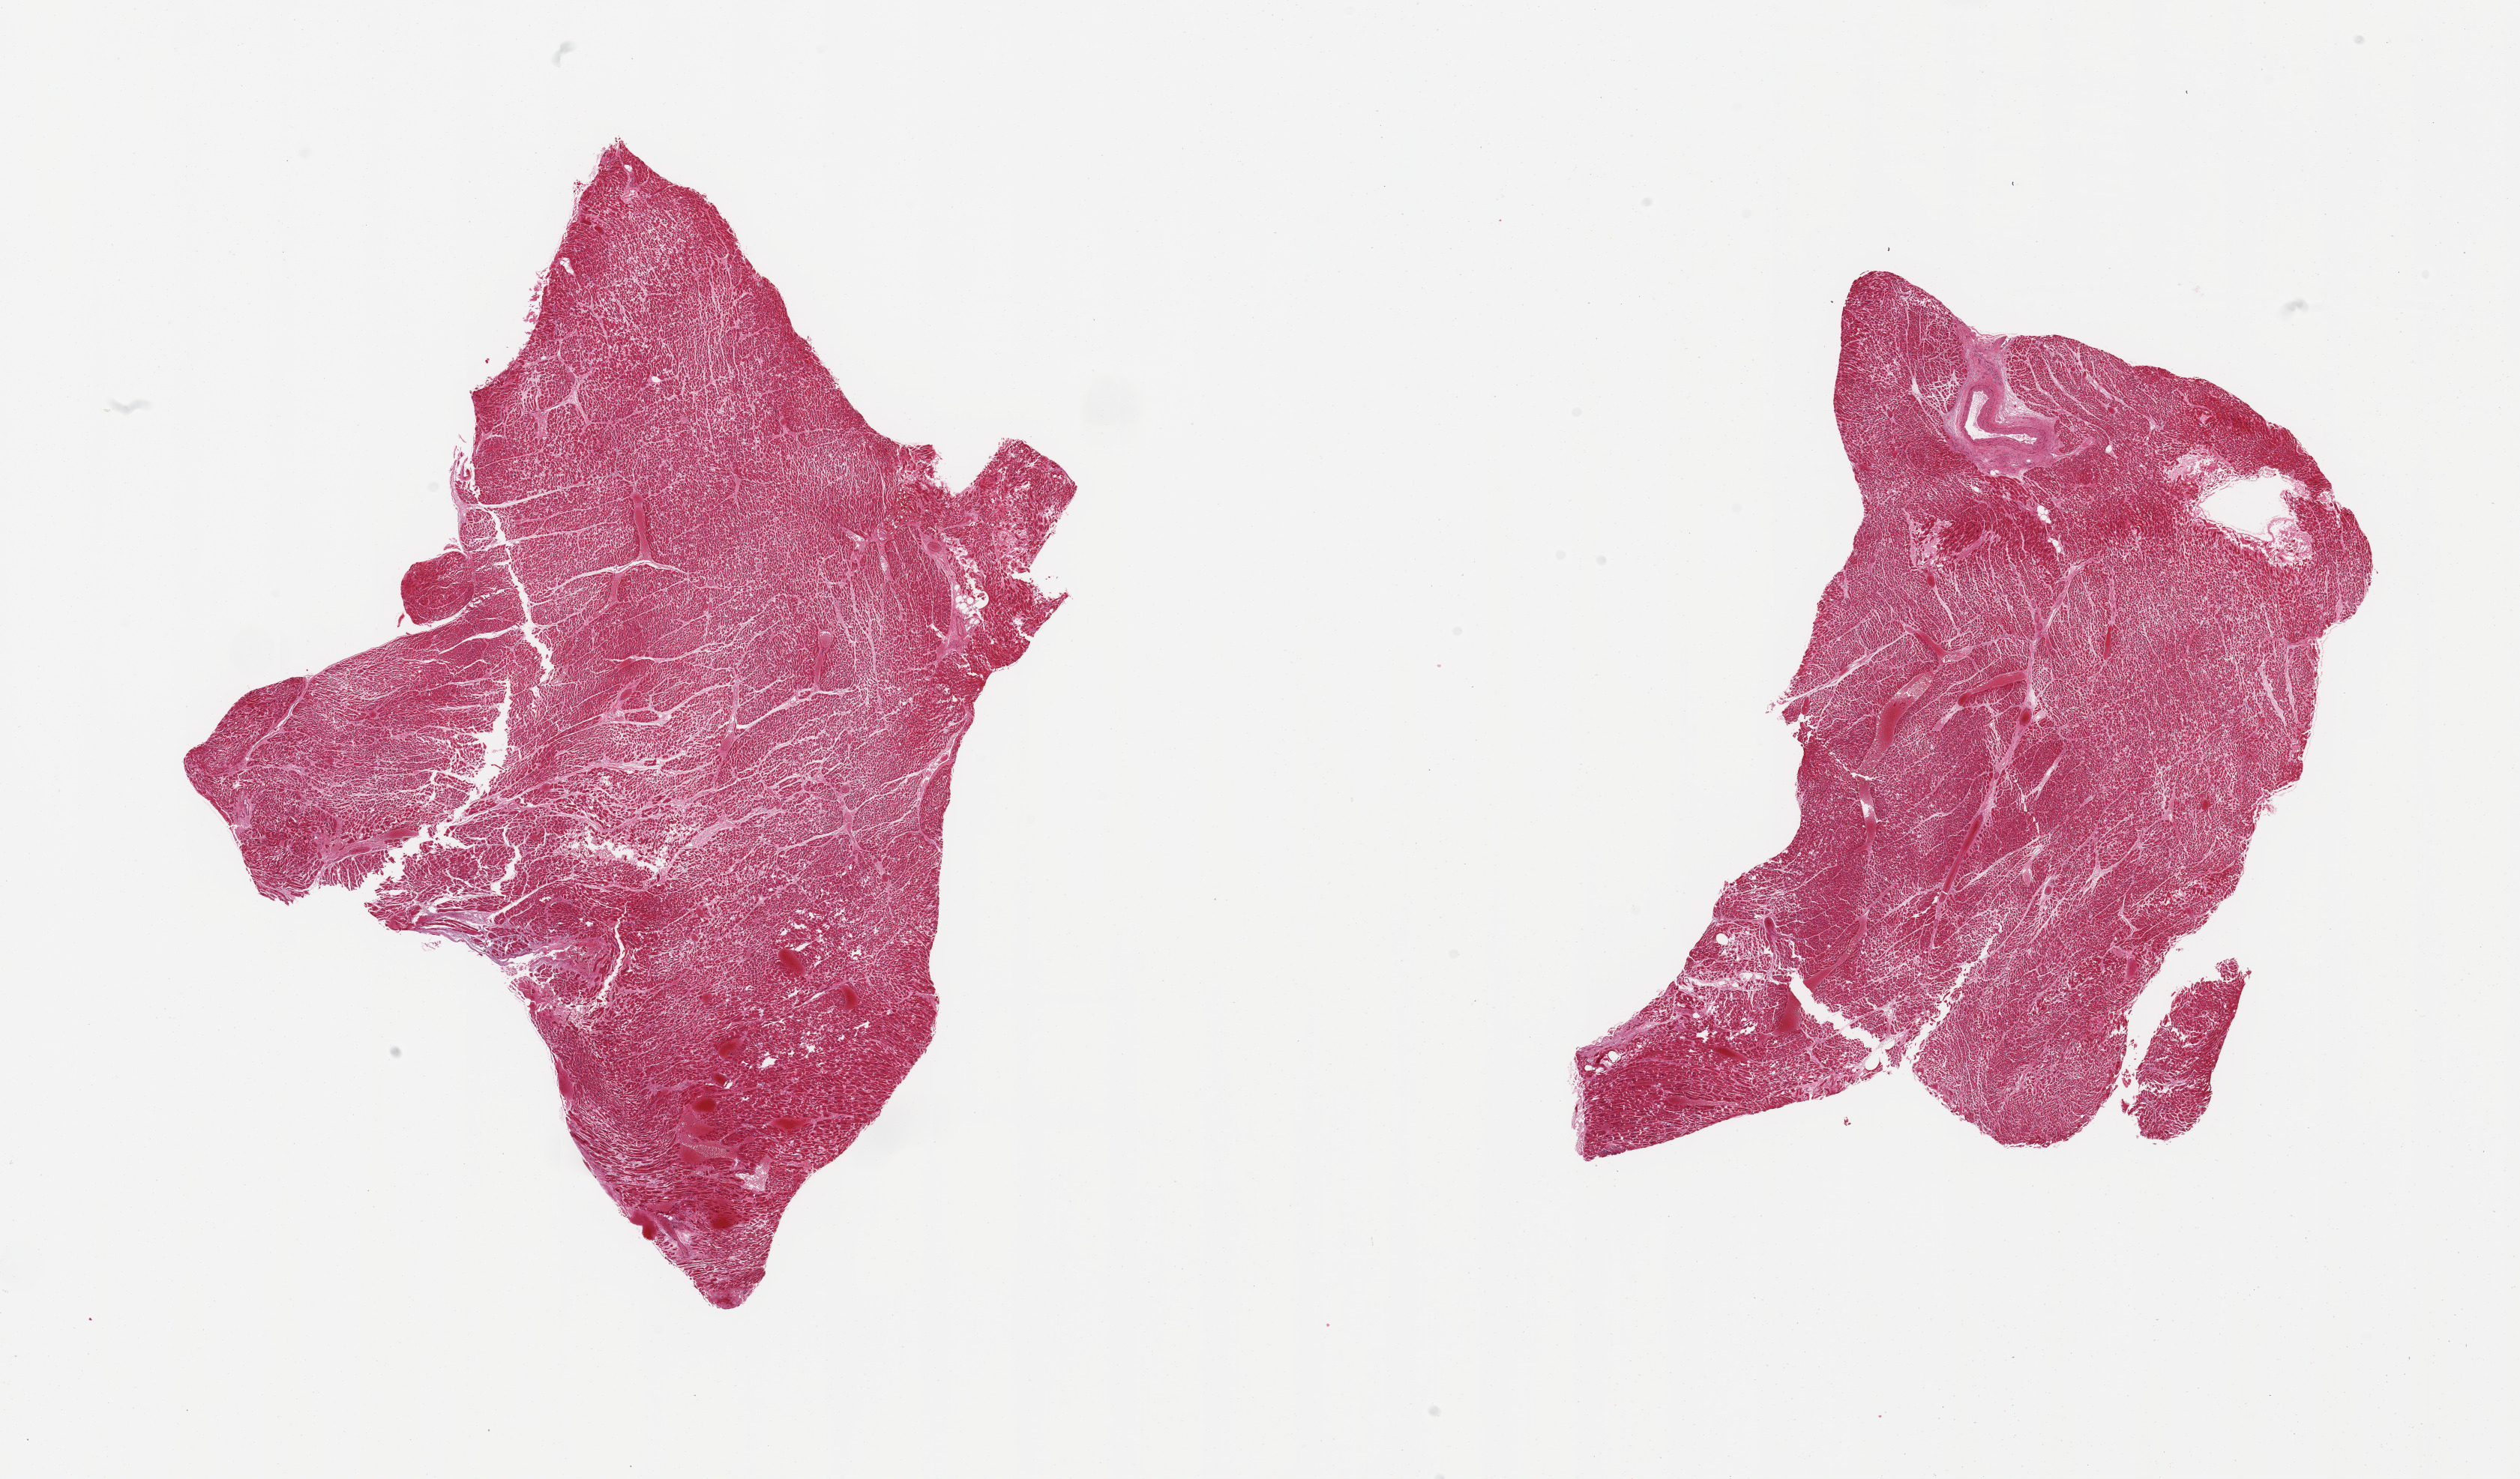
Hematoxylin and eosin (H&E) whole-slide image, whole scanned area (about 26.6 x 15.6 mm) shown as a low-resolution overview, PAXgene-fixed paraffin-embedded (PFPE) section, sampled site (target tissue): heart, donor tissue sample. Donor: female.
* reviewer comment on this tissue sample: 2 pieces, moderate chronic ischemic changes, patchy hyperemia c/w acute infarcts